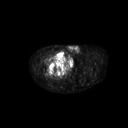
FDG PET of an extremity soft-tissue mass (from a PET/CT study), one axial slice; slice 278 of 311 in the series (ordered by position); 128 × 128 image matrix. Patient: male, 50 years. Case-level facts recorded for this patient, not image findings: histological type: undifferentiated - pleiomorphic; grade: high; site of the primary tumour: right thigh.
Structures marked on this image (expert contour drawn on MRI and transferred to this co-registered scan by the dataset authors):
- gross tumour volume including surrounding oedema: bounding box (x1, y1, x2, y2) in pixels: (48, 51, 66, 68)
- gross tumour volume (mass): (48, 51, 66, 68)